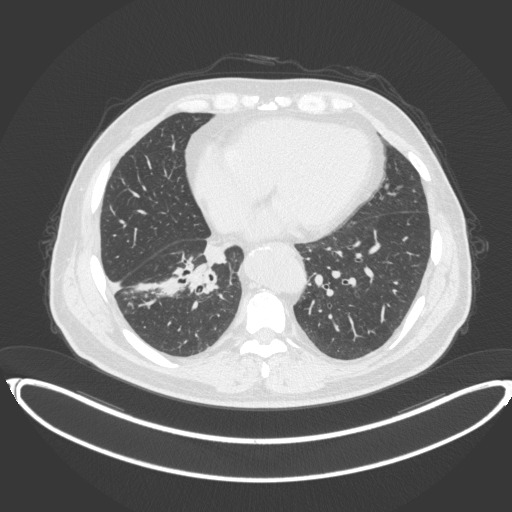
Chest CT, one axial slice; slice 150 of 383 in the series (ordered by position); 120 kVp; lung window (W 1500 / L -600 HU); 512 × 512 image matrix. Male patient, age 61 years. From the clinical record (not read from this slice): clinical TNM (as recorded): T1b N1 M0.
Annotated regions visible in this slice (bounding box drawn by a radiologist):
- lung tumour (recorded histology: squamous cell carcinoma): bounding box <167,257,220,300> (left, top, right, bottom; pixels)